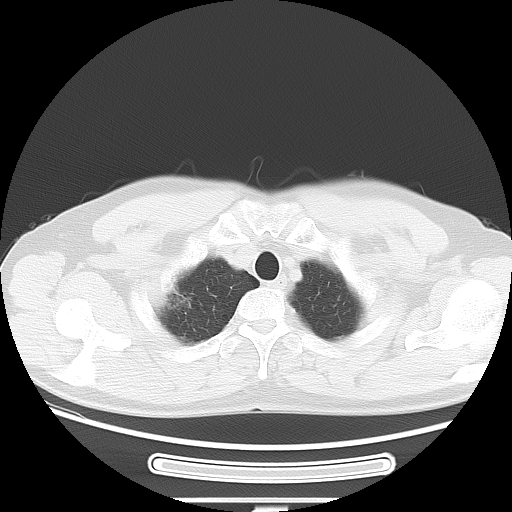
Chest CT, one axial slice. Slice 60 of 68 in the series (ordered by position). Reconstruction kernel LUNG. 120 kVp. Lung window (W 1500 / L -600 HU). 5 mm slice thickness. 512 × 512 image matrix, field of view 382 × 382 mm. Patient: male, 53 years. From the clinical record (not read from this slice): clinical TNM (as recorded): T1c N0 M0; histopathological grade: G2.
Outlined on this slice (bounding box drawn by a radiologist):
- lung tumour (recorded histology: adenocarcinoma): bounding box (x1, y1, x2, y2) in pixels: (157, 280, 207, 322)